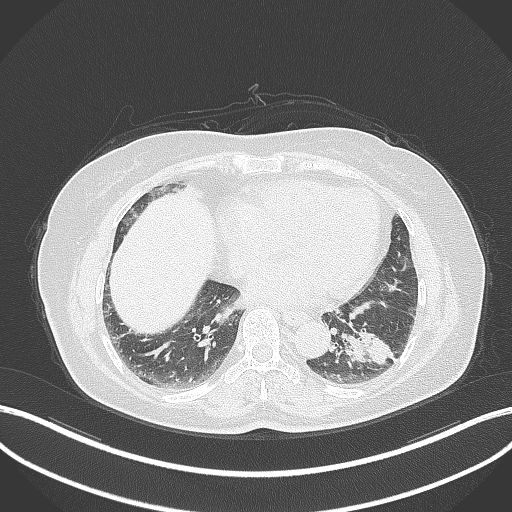
Chest CT, one axial slice; slice 137 of 311 in the series (ordered by position); reconstruction kernel B70f; 120 kVp; lung window (W 1500 / L -600 HU); 1 mm slice thickness; 512 × 512 image matrix, field of view 400 × 400 mm. Patient: female, 59 years. From the clinical record (not read from this slice): clinical TNM (as recorded): T2a N0 M0; histopathological grade: G2-3.
Structures marked on this image (rectangle marked by the reading radiologist):
- lung tumour (recorded histology: adenocarcinoma): bounding box <335,321,394,373> (left, top, right, bottom; pixels)